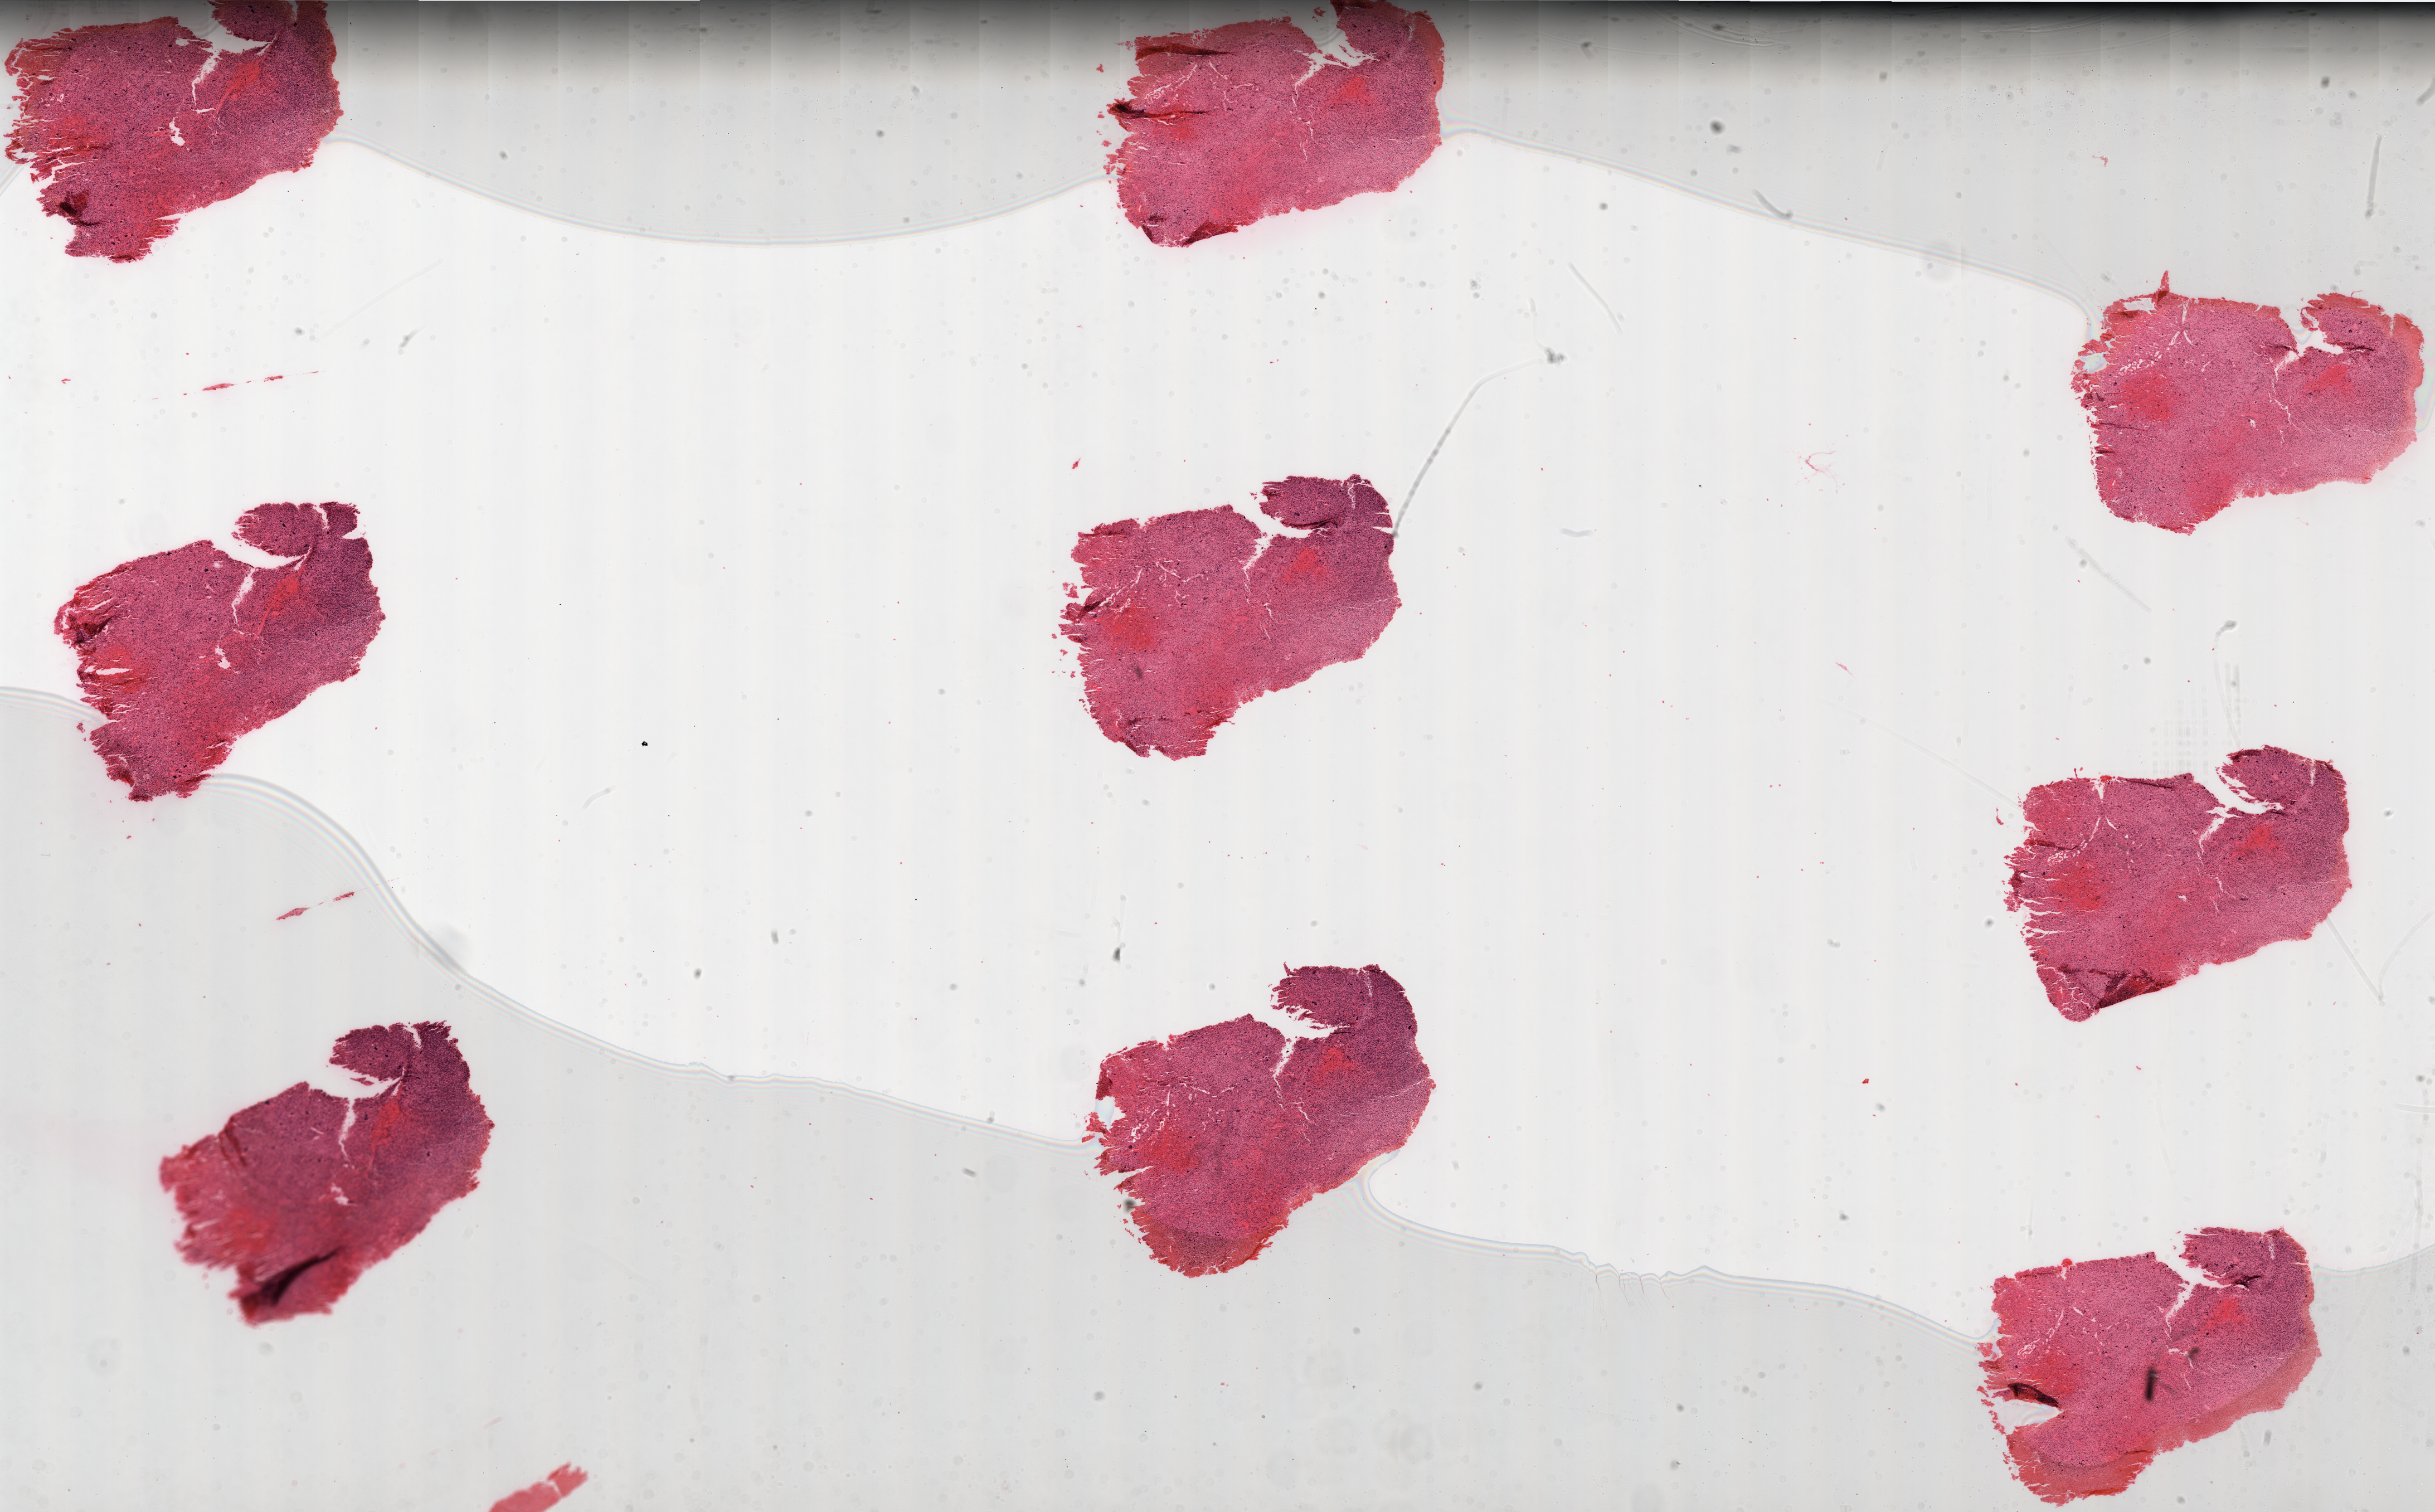
Digitized H&E tissue section (whole slide), whole scanned area (about 35.0 x 21.7 mm, slide scanned at 20x) shown as a low-resolution overview. FFPE section. Primary tumour sample from the brain. Male, age 63 years at initial diagnosis.
* histologic diagnosis: Glioblastoma